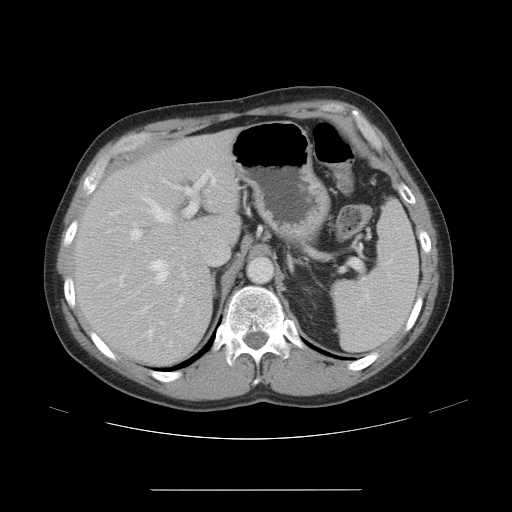
Contrast-enhanced abdominal CT, one axial slice. Position 32 of 48 along the scan axis. 120 kVp. Soft-tissue window (W 400 / L 40 HU). 5 mm slice thickness. 512 × 512 image matrix. Male patient, age 56 years. From the clinical record (not read from this slice): diagnosis: colorectal cancer liver metastases, imaged before liver resection; multiple liver metastases: yes; largest metastasis: 1.8 cm.
Structures marked on this image (outlined manually by an expert reader):
- hepatic veins: bounding box <101,184,172,341> (left, top, right, bottom; pixels)
- liver: <77,133,238,363>
- planned liver remnant (the part of the liver to remain after resection): <77,133,238,363>
- portal vein (with intrahepatic branches): <130,168,217,307>